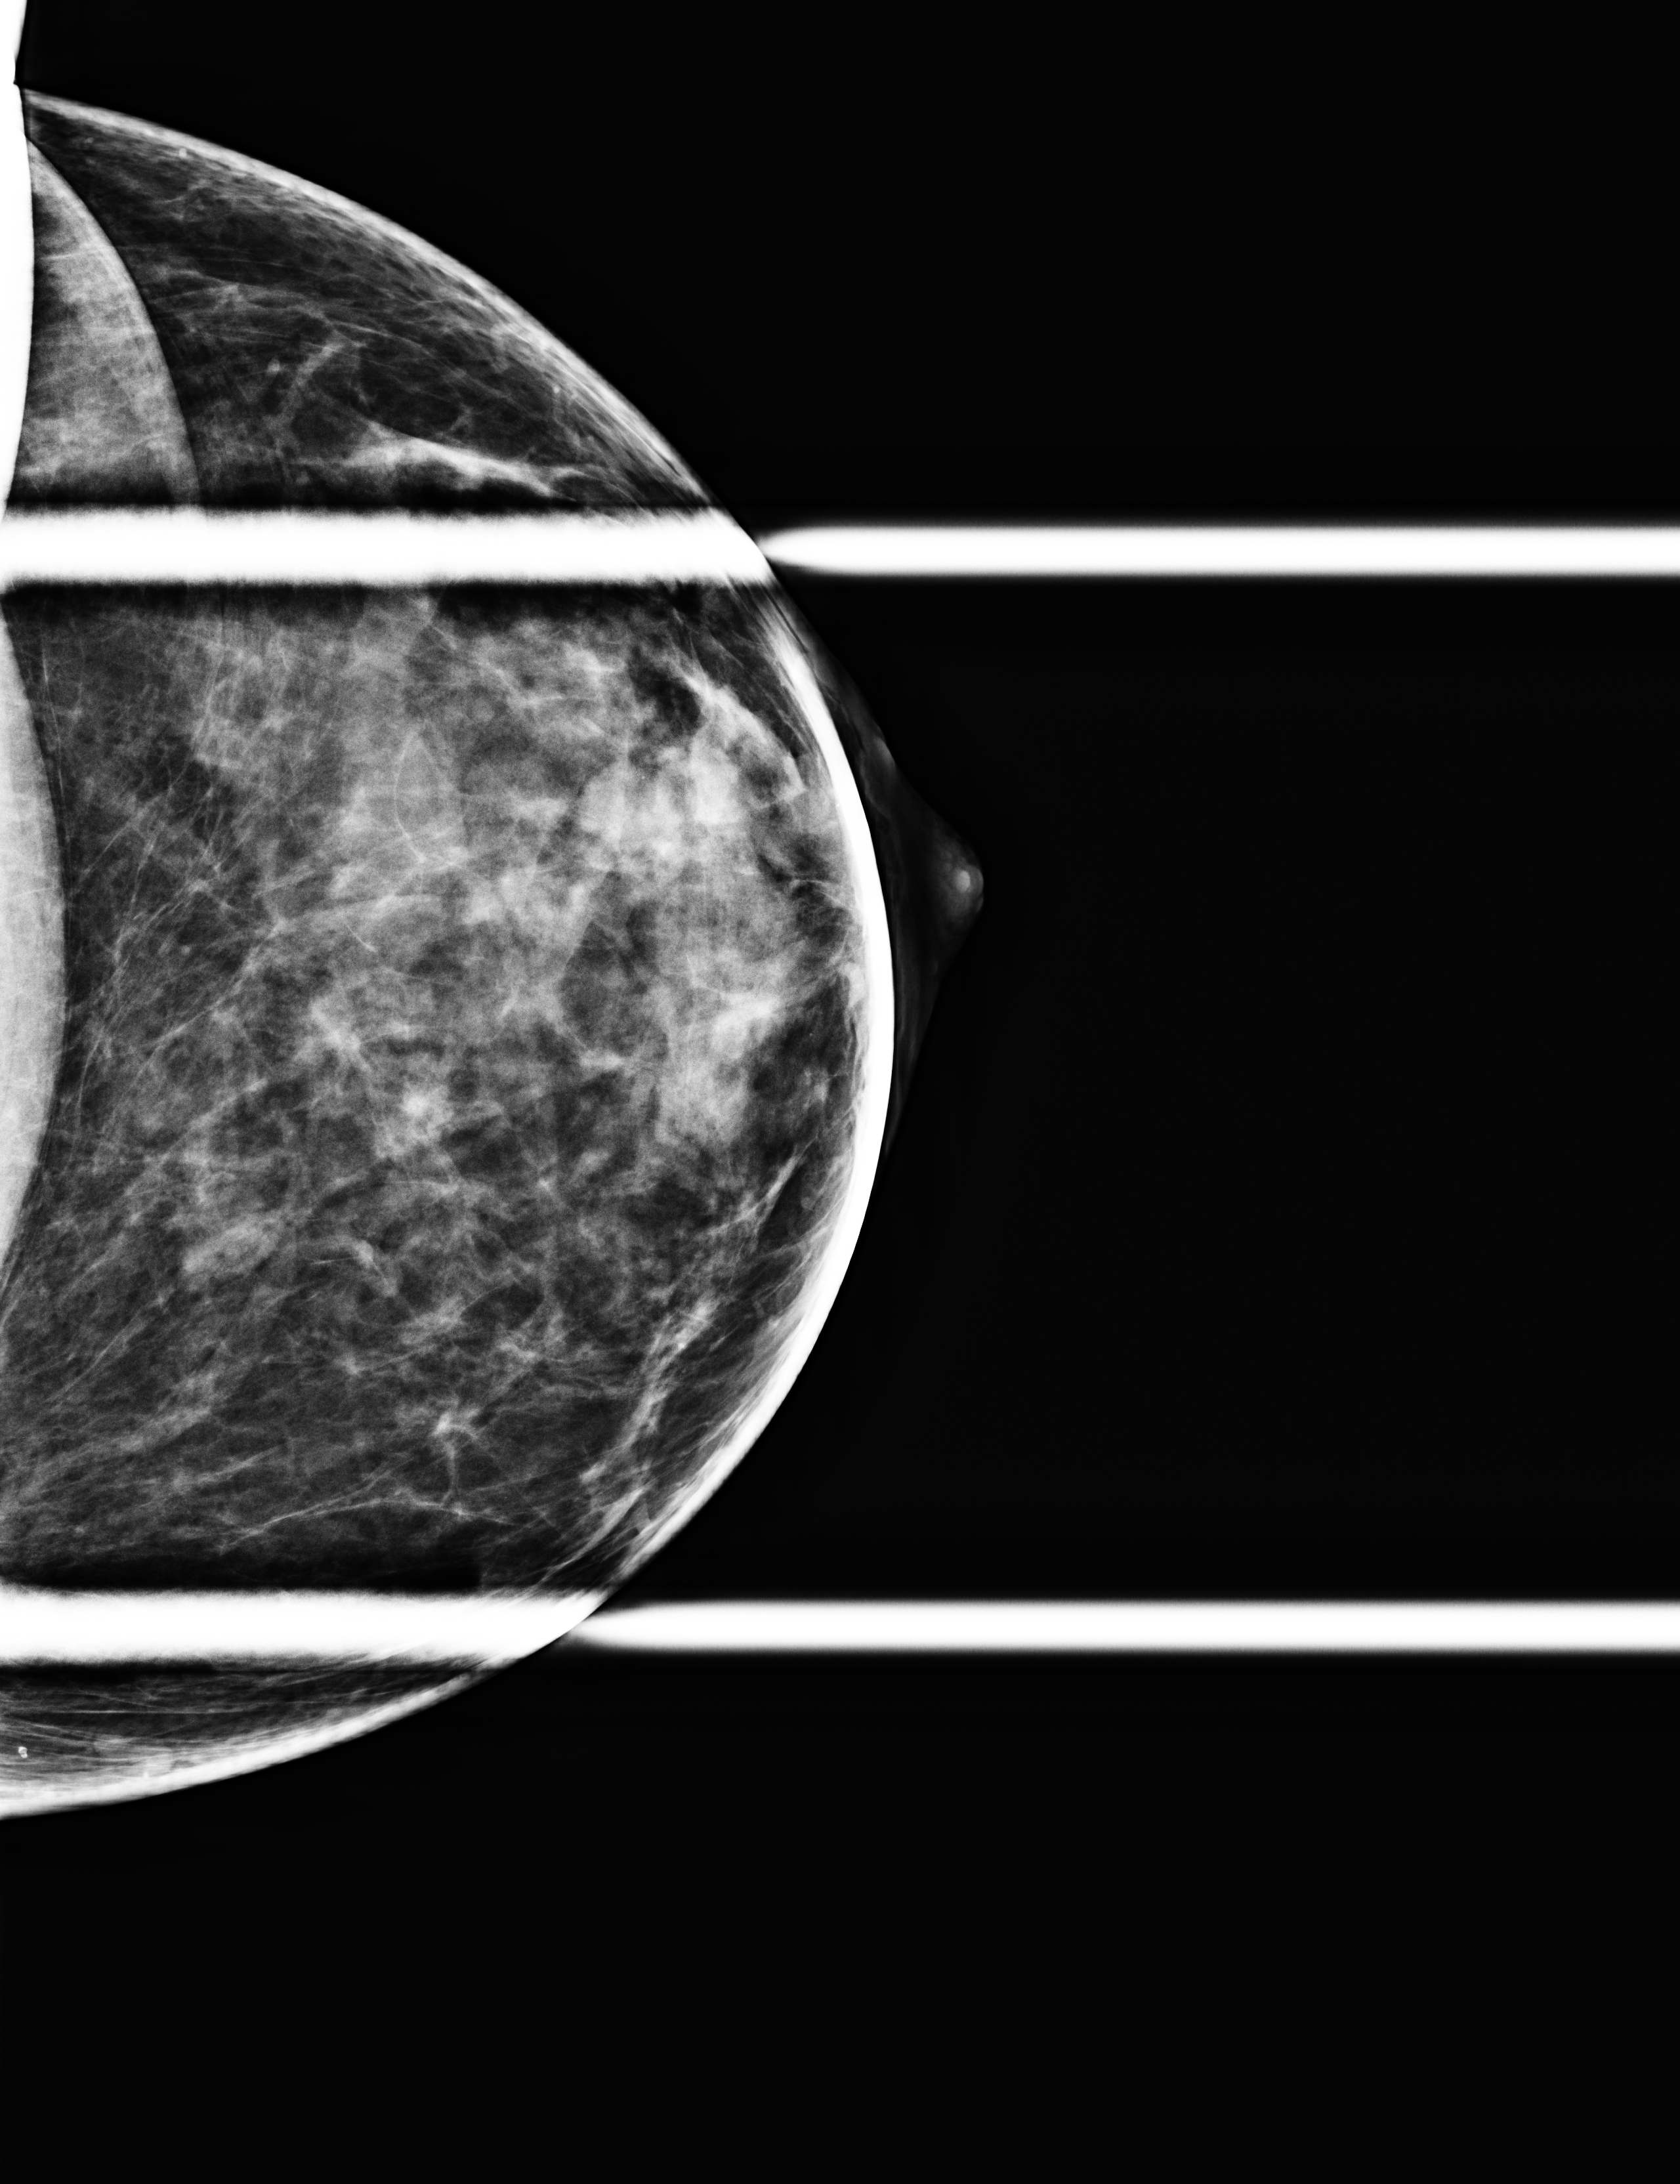
Additional (diagnostic) view. Patient: female, 45 years.
Image type: full-field digital mammogram. Breast: left. Projection: cranio-caudal projection, spot compression.